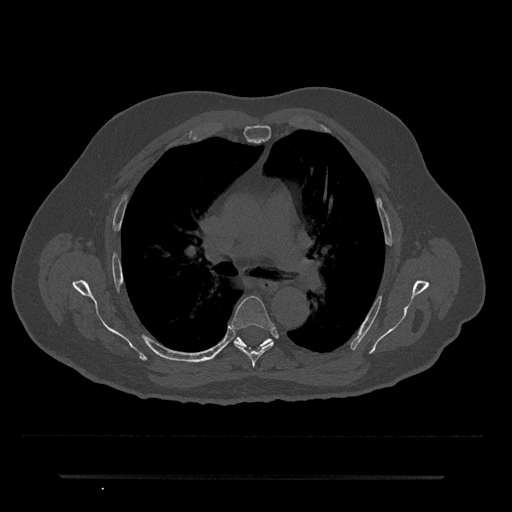
CT including the spine, one axial slice. Position 467 of 797 along the scan axis. Reconstruction kernel Br40s/3. Bone window (W 1800 / L 400 HU). 0.5 mm slice thickness. 512 × 512 image matrix, field of view 437 × 437 mm. Male patient, age 69 years. From the clinical record (not read from this slice): primary cancer: prostate.
Structures marked on this image (semi-automatic segmentation, software-assisted and operator-edited):
- T5 vertebra: bounding box <230,296,274,367> (left, top, right, bottom; pixels)
- T6 vertebra: <235,337,271,347>